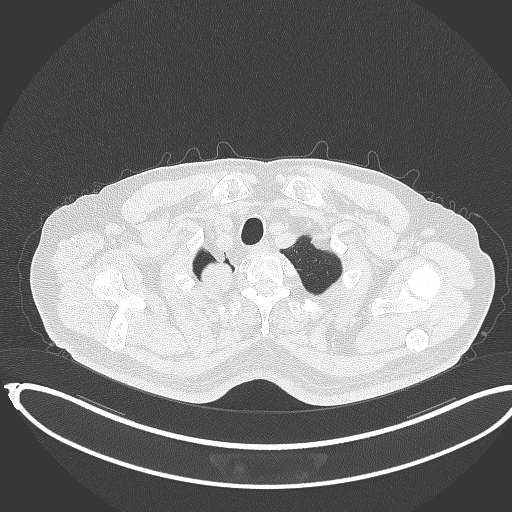
Chest CT, one axial slice. Position 342 of 403 along the scan axis. 120 kVp. Lung window (W 1500 / L -600 HU). 1 mm slice thickness. 512 × 512 image matrix. Patient: male, 68 years. Case-level facts recorded for this patient, not image findings: clinical TNM (as recorded): T2a N0 M0.
Annotated regions visible in this slice (bounding box drawn by a radiologist):
- lung tumour (recorded histology: adenocarcinoma): bounding box (x1, y1, x2, y2) in pixels: (199, 251, 237, 297)